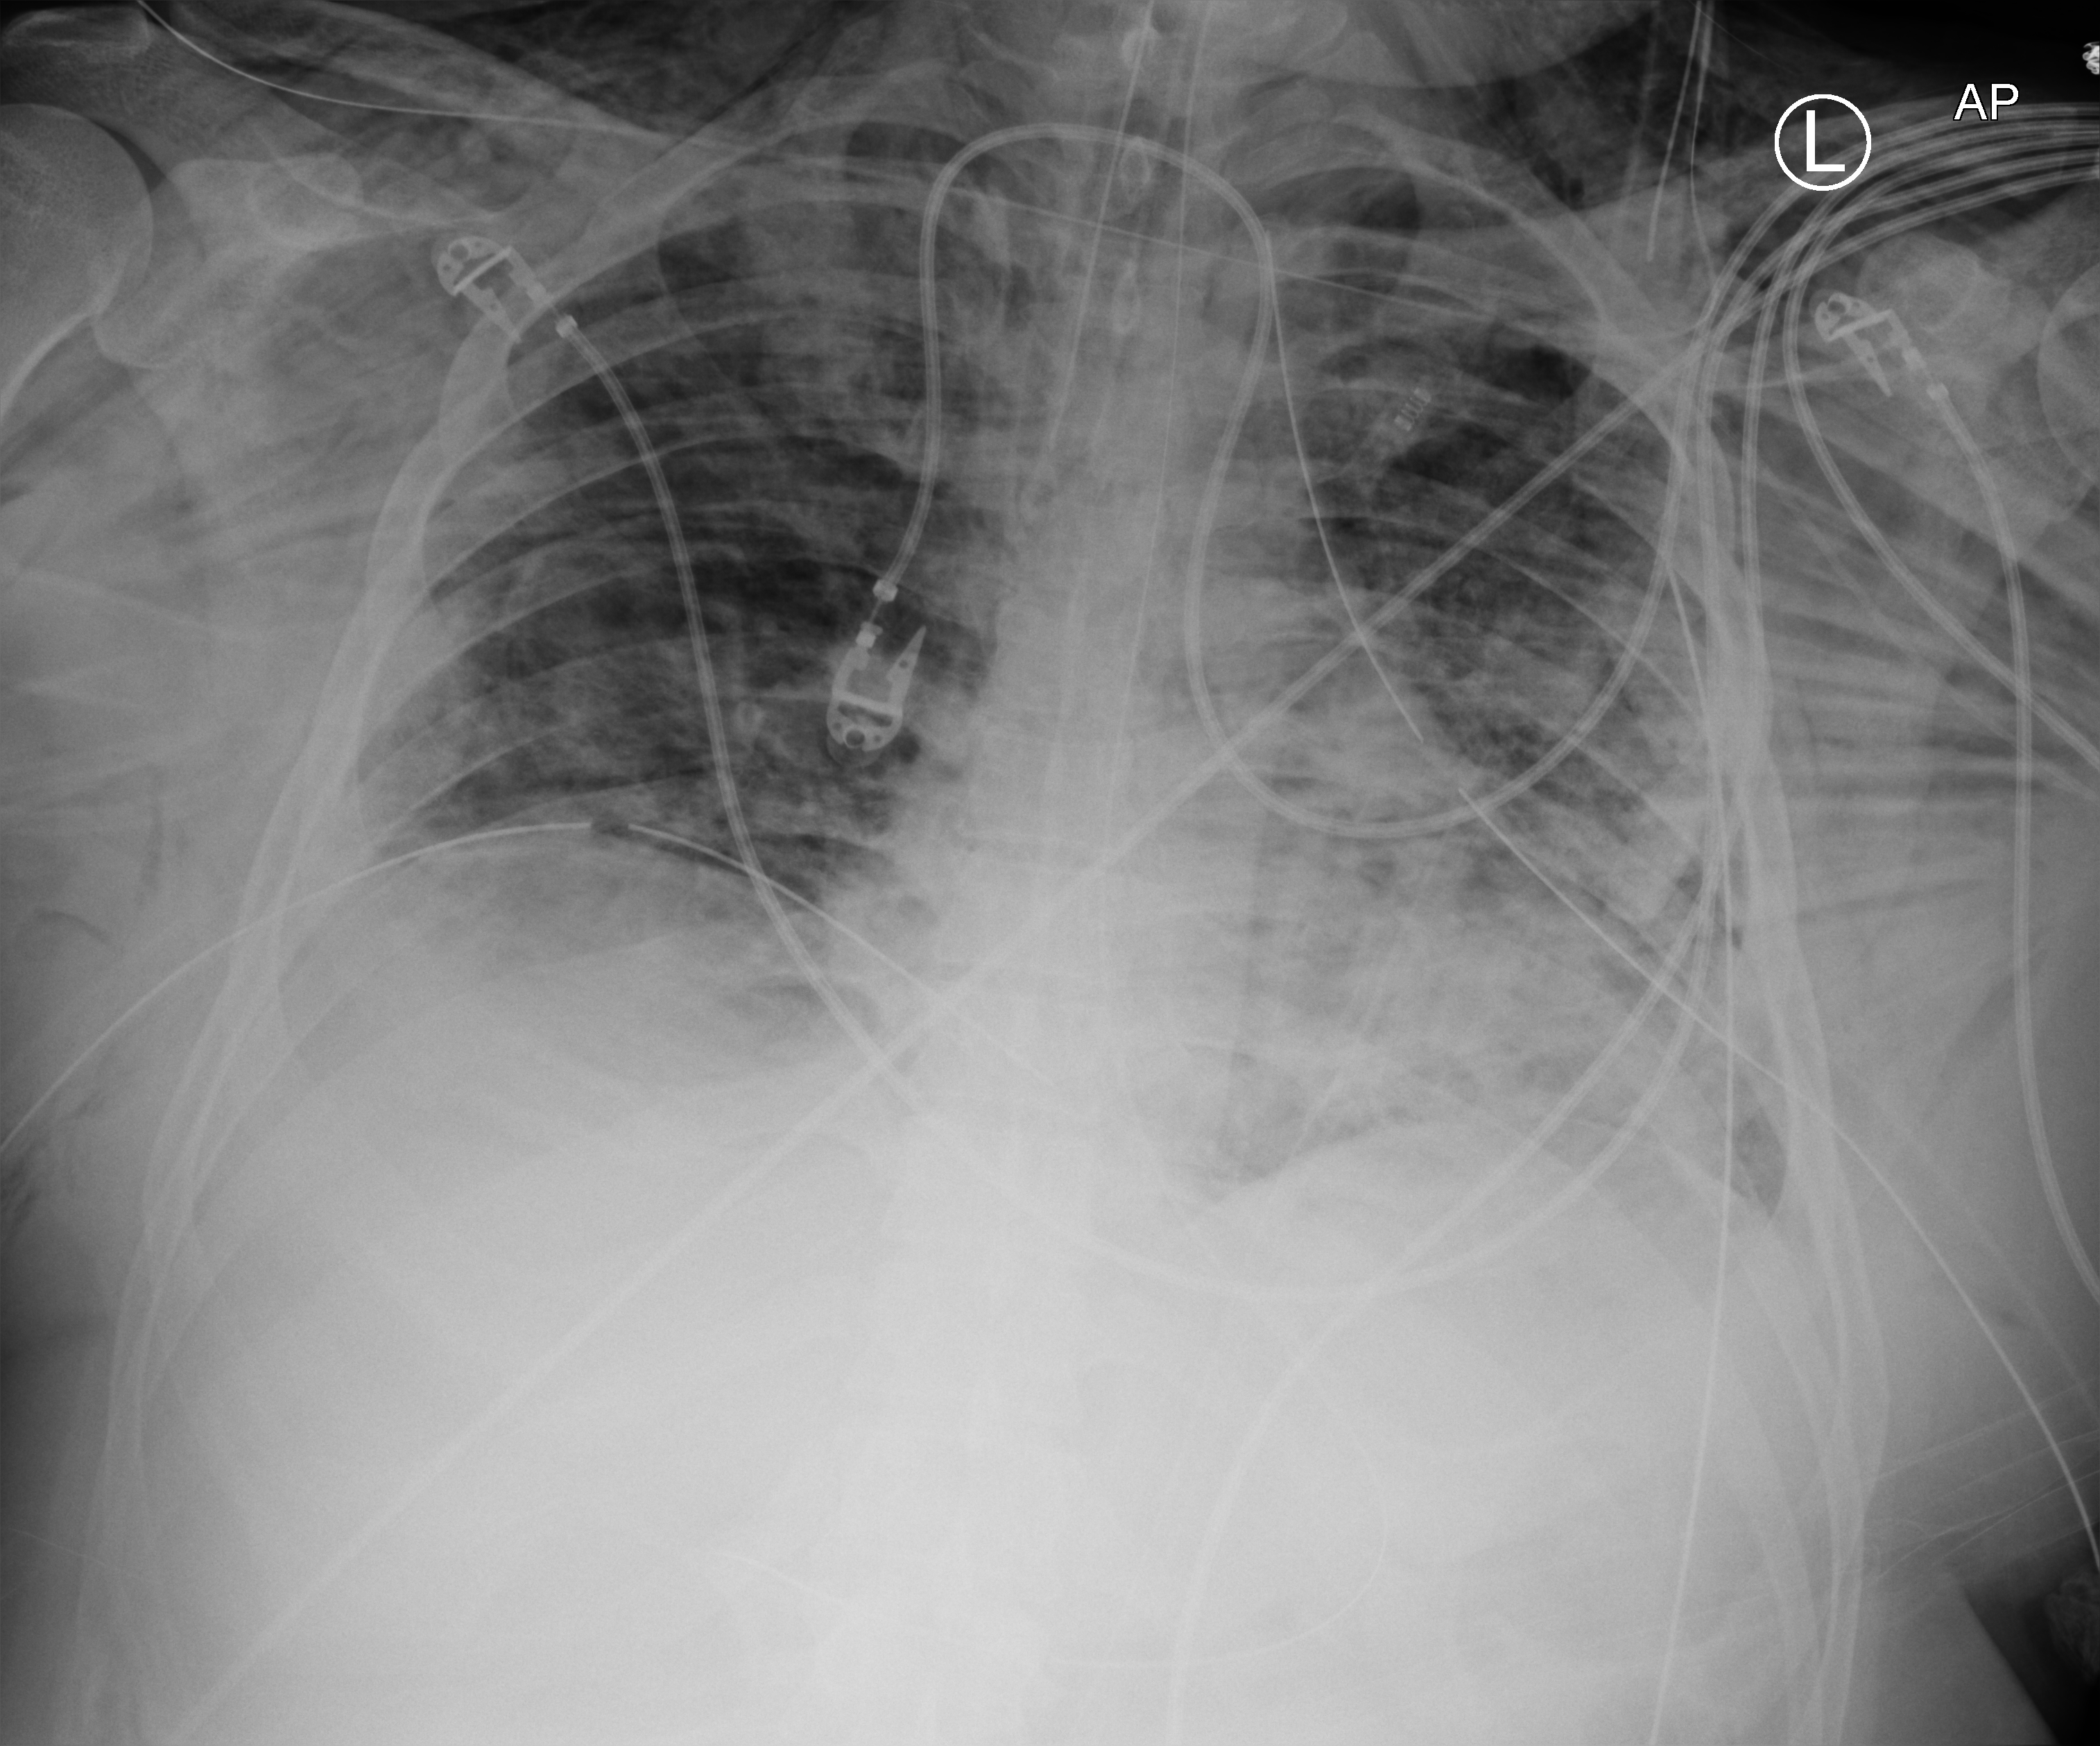
Portable chest radiograph, anteroposterior (AP) projection. Male patient hospitalised with COVID-19, age 18–59 years.
Admission-level facts for this patient (not findings on this image; timing relative to this image not recorded): admitted to intensive care during this hospital stay: yes; mechanically ventilated during this hospital stay: yes.